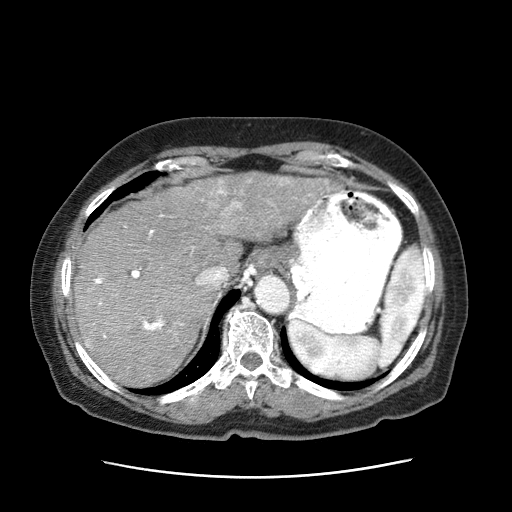
Contrast-enhanced abdominal CT (liver protocol), one axial slice. Position 52 of 63 along the scan axis. Intravenous contrast given. Soft-tissue window (W 400 / L 40 HU). 2.5 mm slice thickness. 512 × 512 image matrix, field of view 360 × 360 mm. Patient: female, 79 years. From the clinical record (not read from this slice): diagnosis: hepatocellular carcinoma (patient treated with transarterial chemoembolisation; whether this scan precedes or follows treatment is not stated here); TNM stage (as recorded): Stage-II; Child-Pugh class: B; tumour nodularity: multinodular; tumour size: 5 cm.
Structures marked on this image (semi-automatically segmented with operator editing):
- abdominal aorta: box from (x=255, y=276) to (x=290, y=314) px
- liver parenchyma outside the tumour (the mass and vessels are separate outlines, so this box may not span the whole liver): (x=76, y=177)–(x=244, y=389)
- mass: (x=93, y=170)–(x=332, y=313)
- liver vessels: (x=93, y=197)–(x=294, y=338)